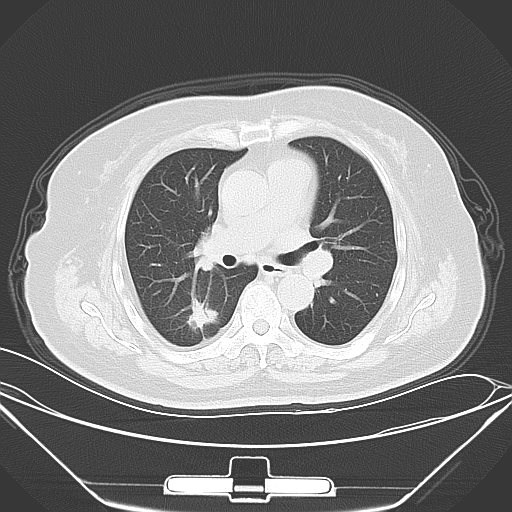
Chest CT, one axial slice; slice 37 of 64 in the series (ordered by position); lung window (W 1500 / L -600 HU); 512 × 512 image matrix, field of view 396 × 396 mm. Patient: female, 70 years. Case-level facts recorded for this patient, not image findings: clinical TNM (as recorded): T2 N0 M3.
Structures marked on this image (rectangle marked by the reading radiologist):
- lung tumour (recorded histology: adenocarcinoma): bounding box (x1, y1, x2, y2) in pixels: (180, 293, 226, 339)